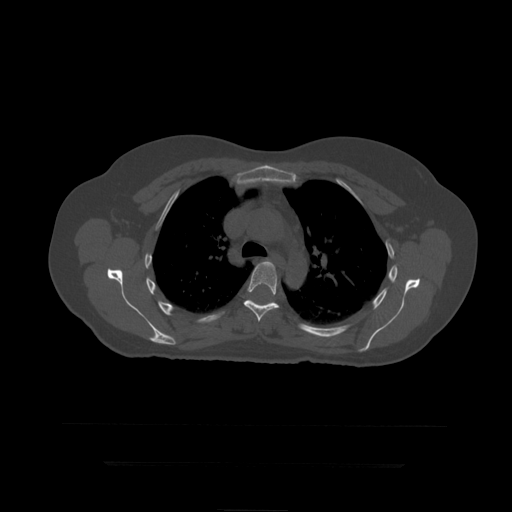
CT including the spine, one axial slice; position 319 of 399 along the scan axis; reconstruction kernel STANDARD; bone window (W 1800 / L 400 HU); 1.25 mm slice thickness; 512 × 512 image matrix, field of view 450 × 450 mm. Patient age 41 years. Case-level facts recorded for this patient, not image findings: primary cancer: breast.
Structures marked on this image (semi-automatically segmented with operator editing):
- T6 vertebra: box from (x=244, y=261) to (x=280, y=322) px
- T7 vertebra: (x=248, y=300)–(x=275, y=304)